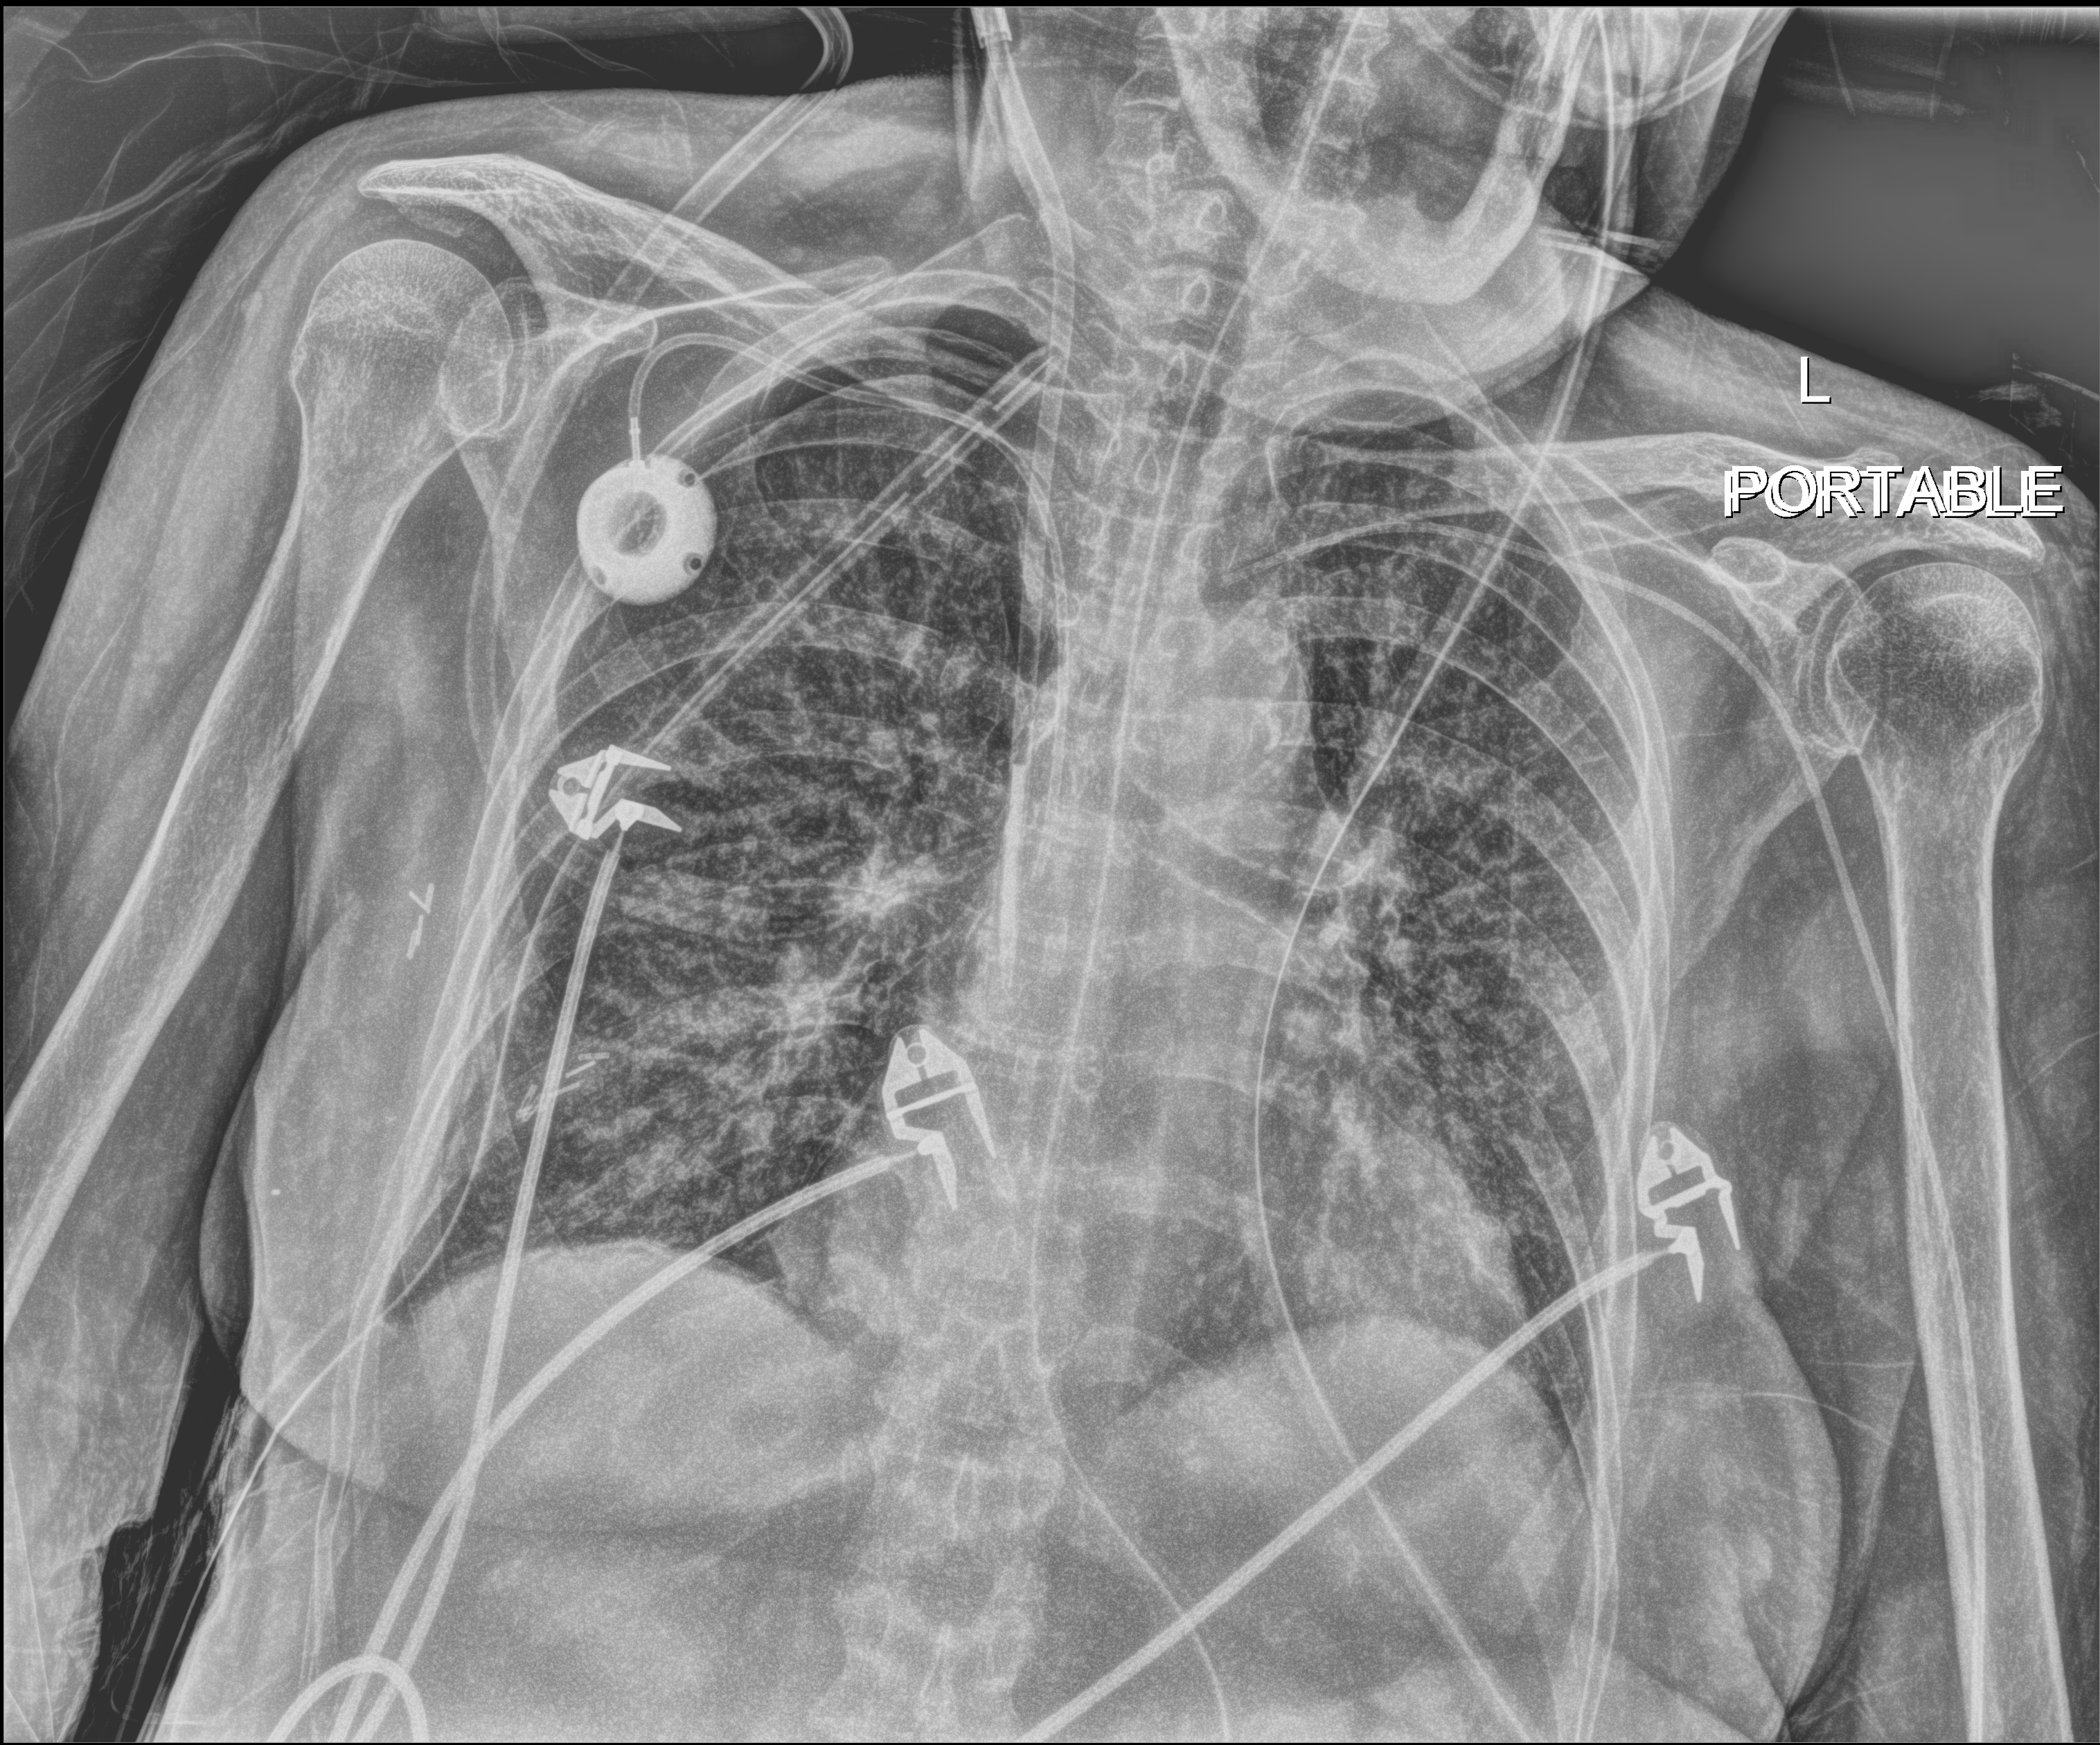
Chest radiograph (digital radiography). Patient hospitalised with COVID-19; female, aged 60–74 years.
Admission-level facts for this patient (not findings on this image; timing relative to this image not recorded):
- admitted to intensive care during this hospital stay: yes
- mechanically ventilated during this hospital stay: yes
- length of hospital stay: 43 days